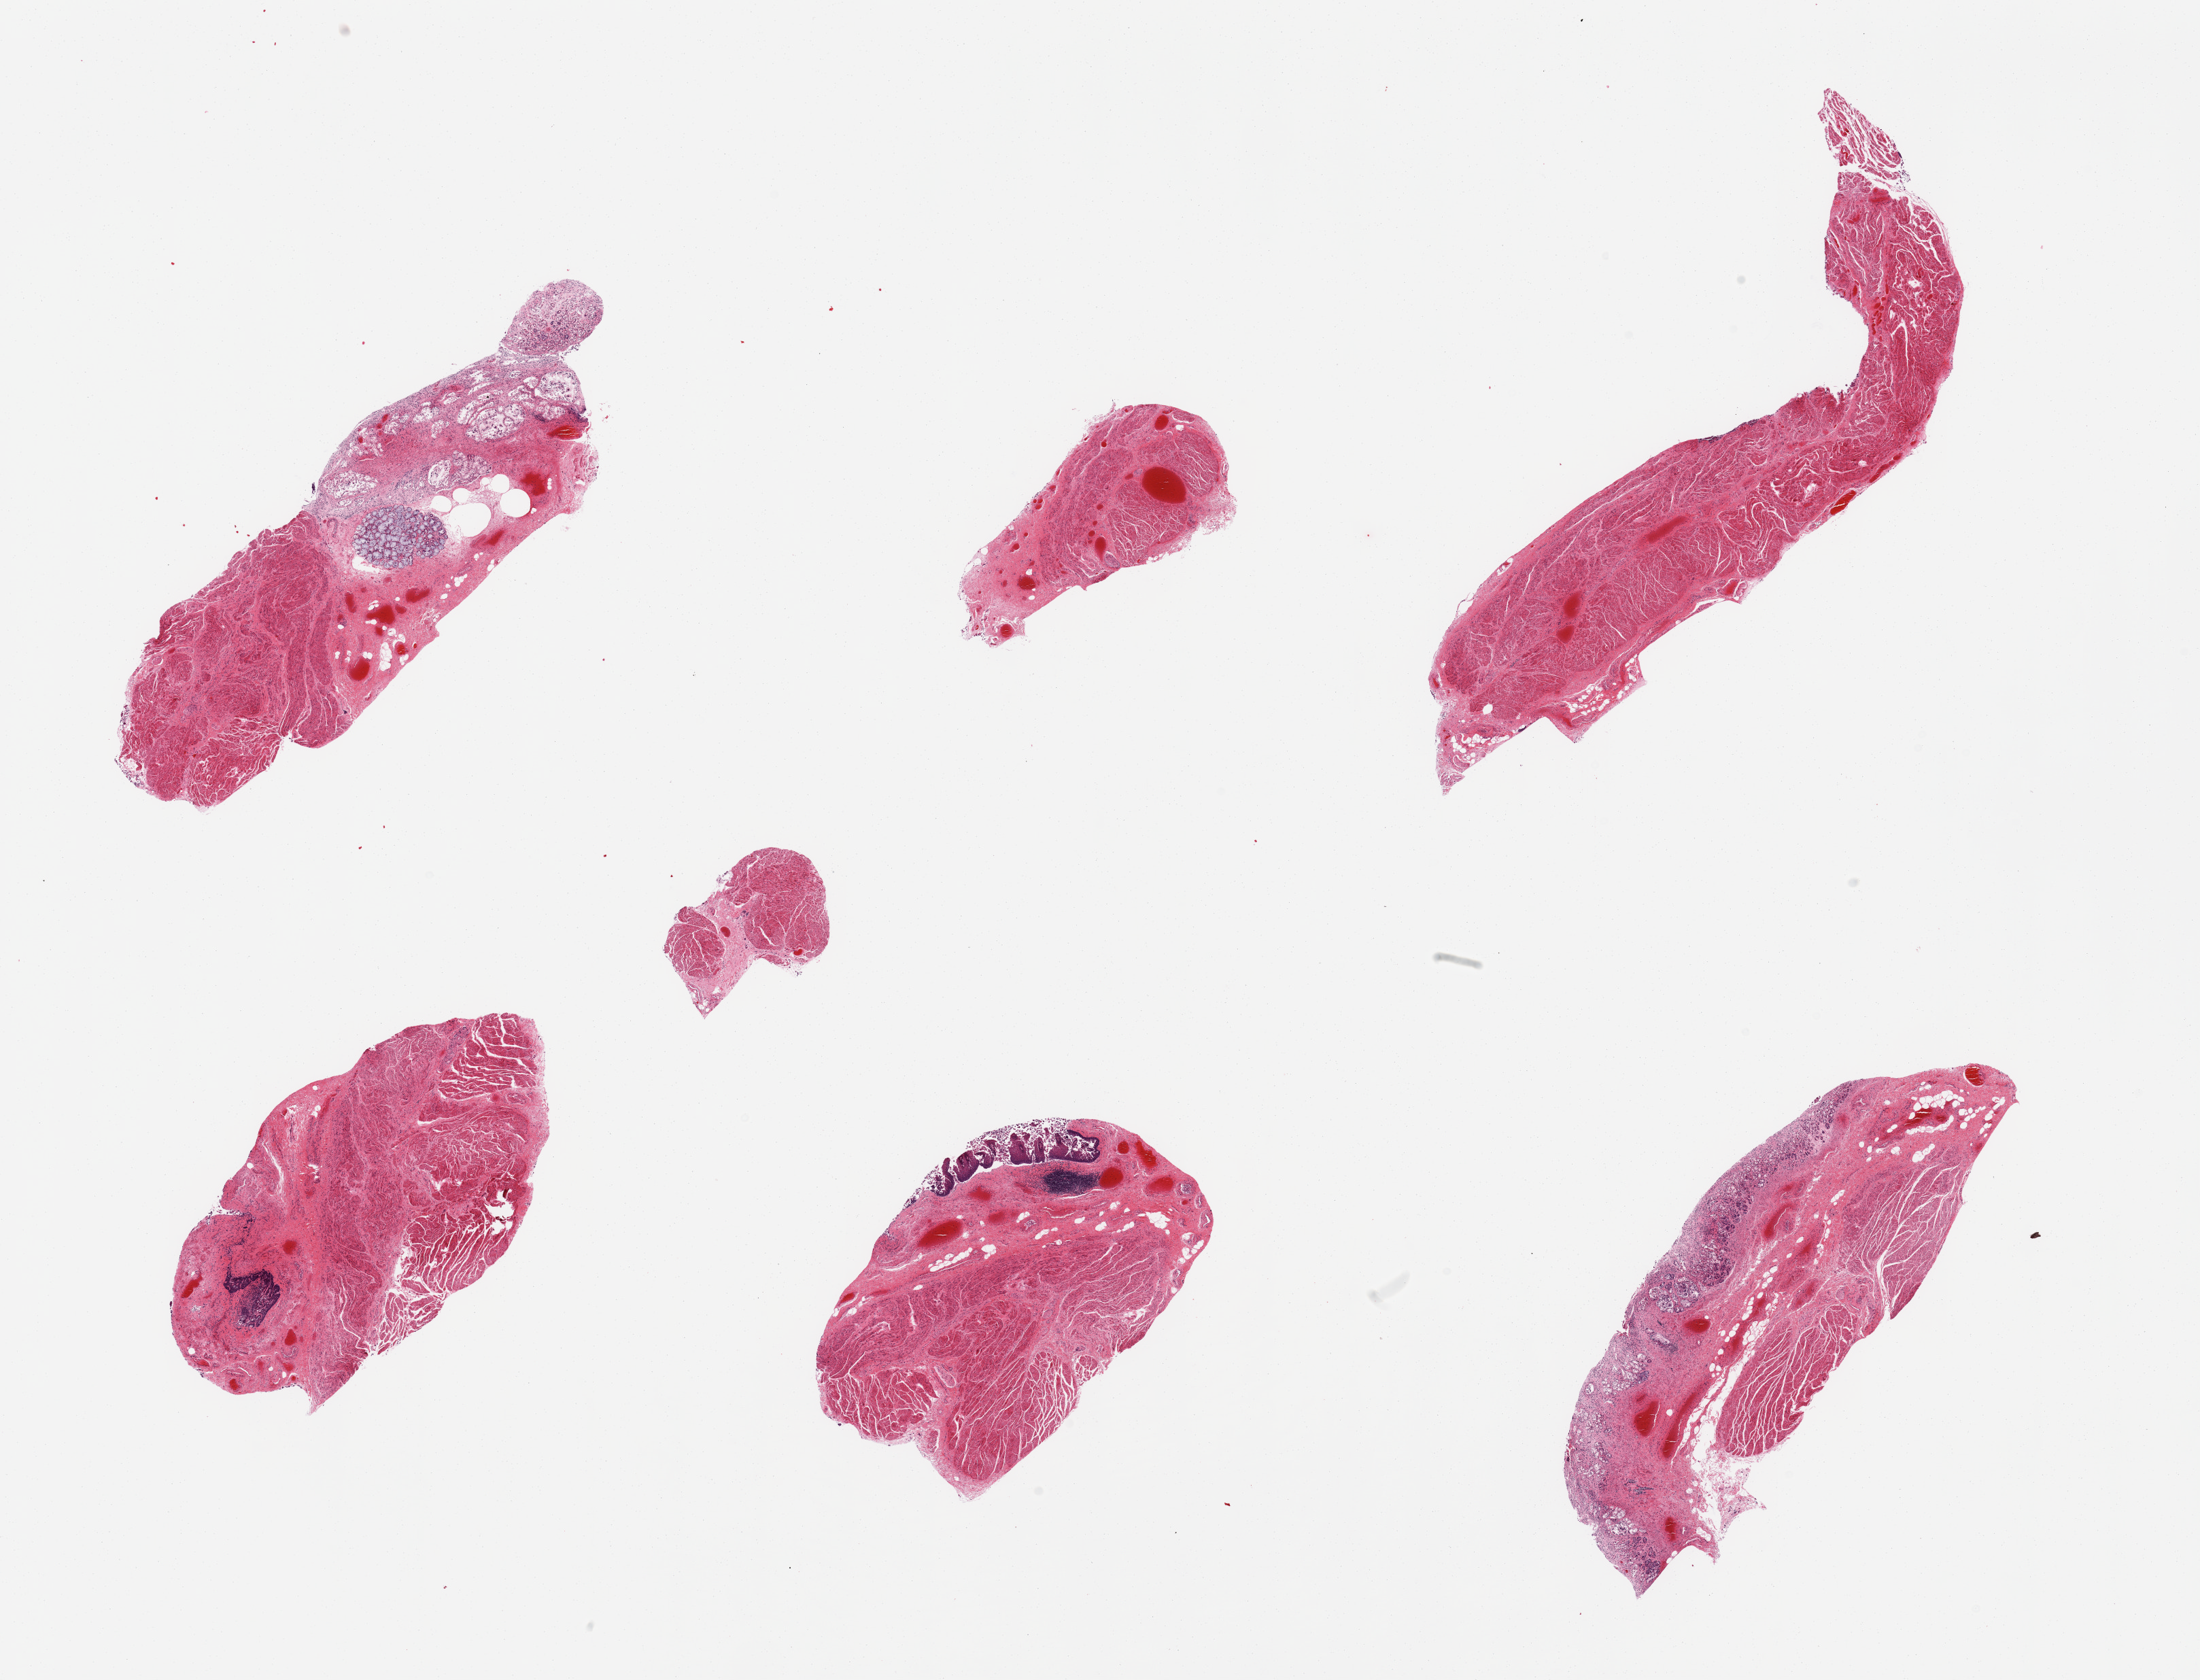
H&E whole-slide image — a low-resolution overview of the entire scanned area, about 25.6 x 19.5 mm (acquisition: 20x scan). PAXgene-fixed, paraffin-embedded tissue. Sampled site (target tissue): gastroesophageal junction. Donor tissue sample. Donor sex: male.
- pathologist's review note for this sample: 7 pieces, muscularis (target) and squamous and gastric mucosa (not target, incorrect region)